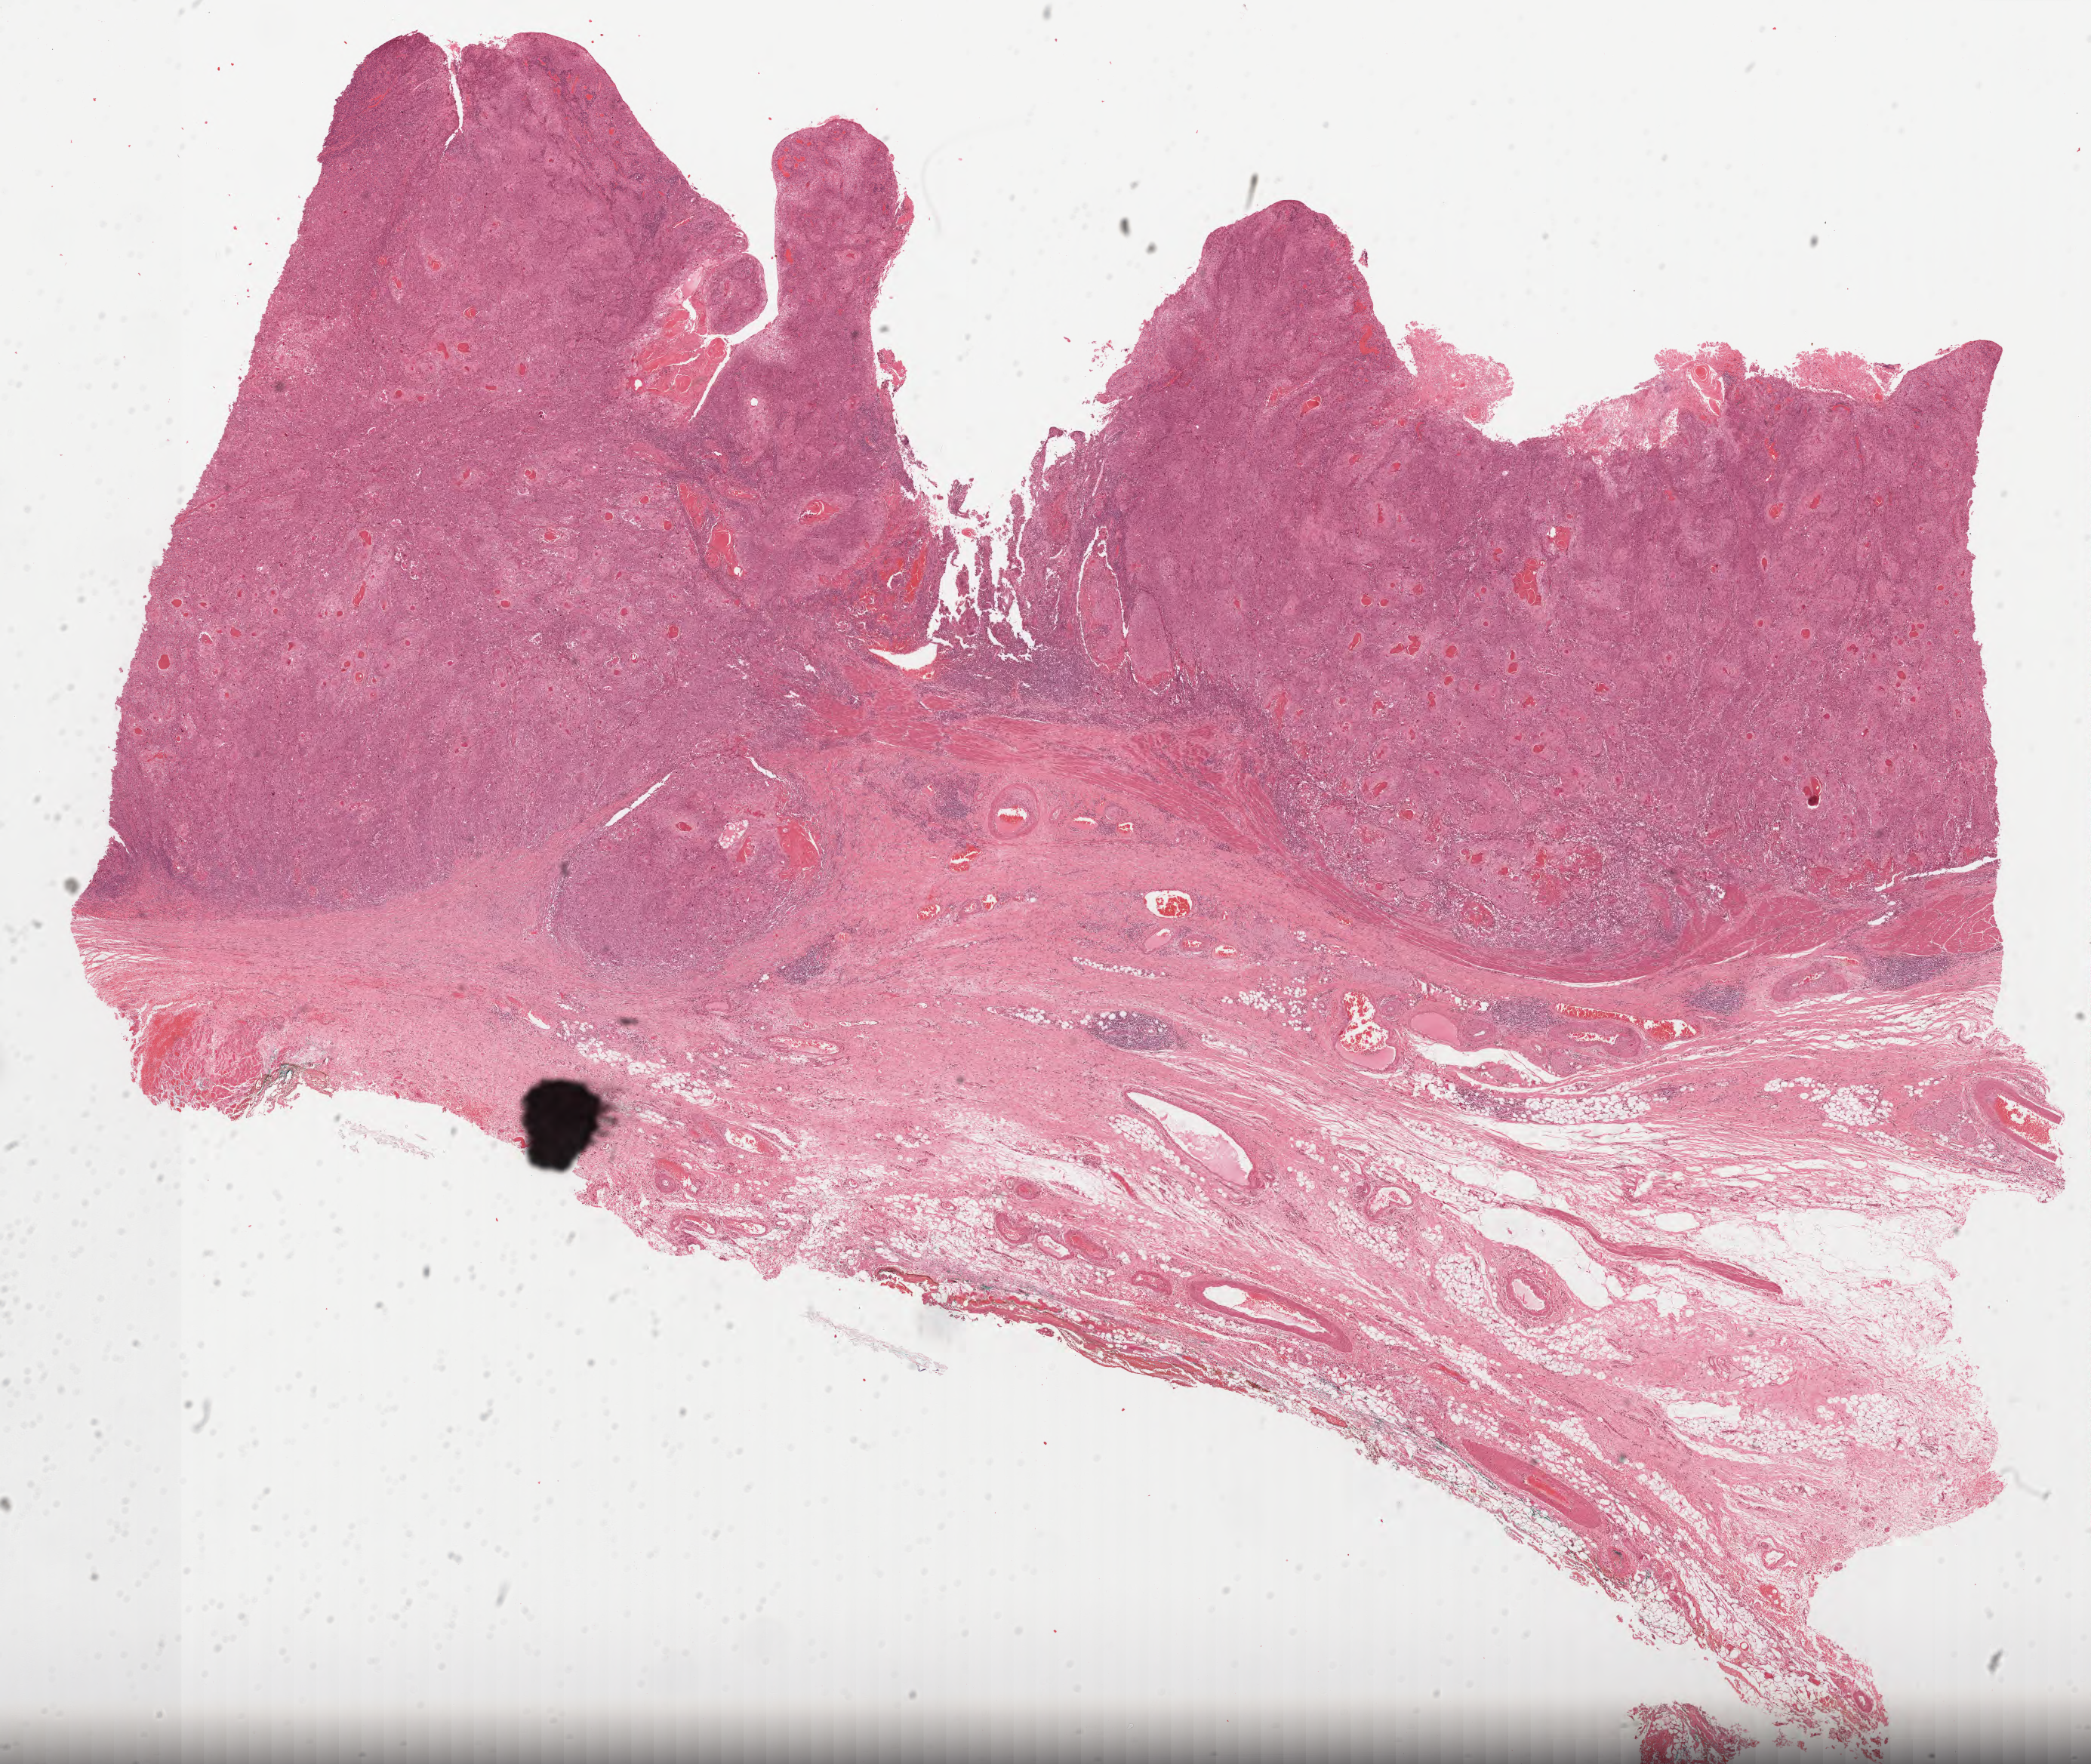
Whole-slide histology image, Hematoxylin and eosin (H&E) stained, whole scanned area (about 22.3 x 18.8 mm) shown as a low-resolution overview, formalin-fixed paraffin-embedded (FFPE) diagnostic section, primary tumour sample from the esophagus. Patient: female, age at initial diagnosis 51 years. Histologic grade: G1 (well differentiated).
Histologic diagnosis: Squamous cell carcinoma, NOS (lower third of esophagus). AJCC pathologic stage: IIA (6th edition).